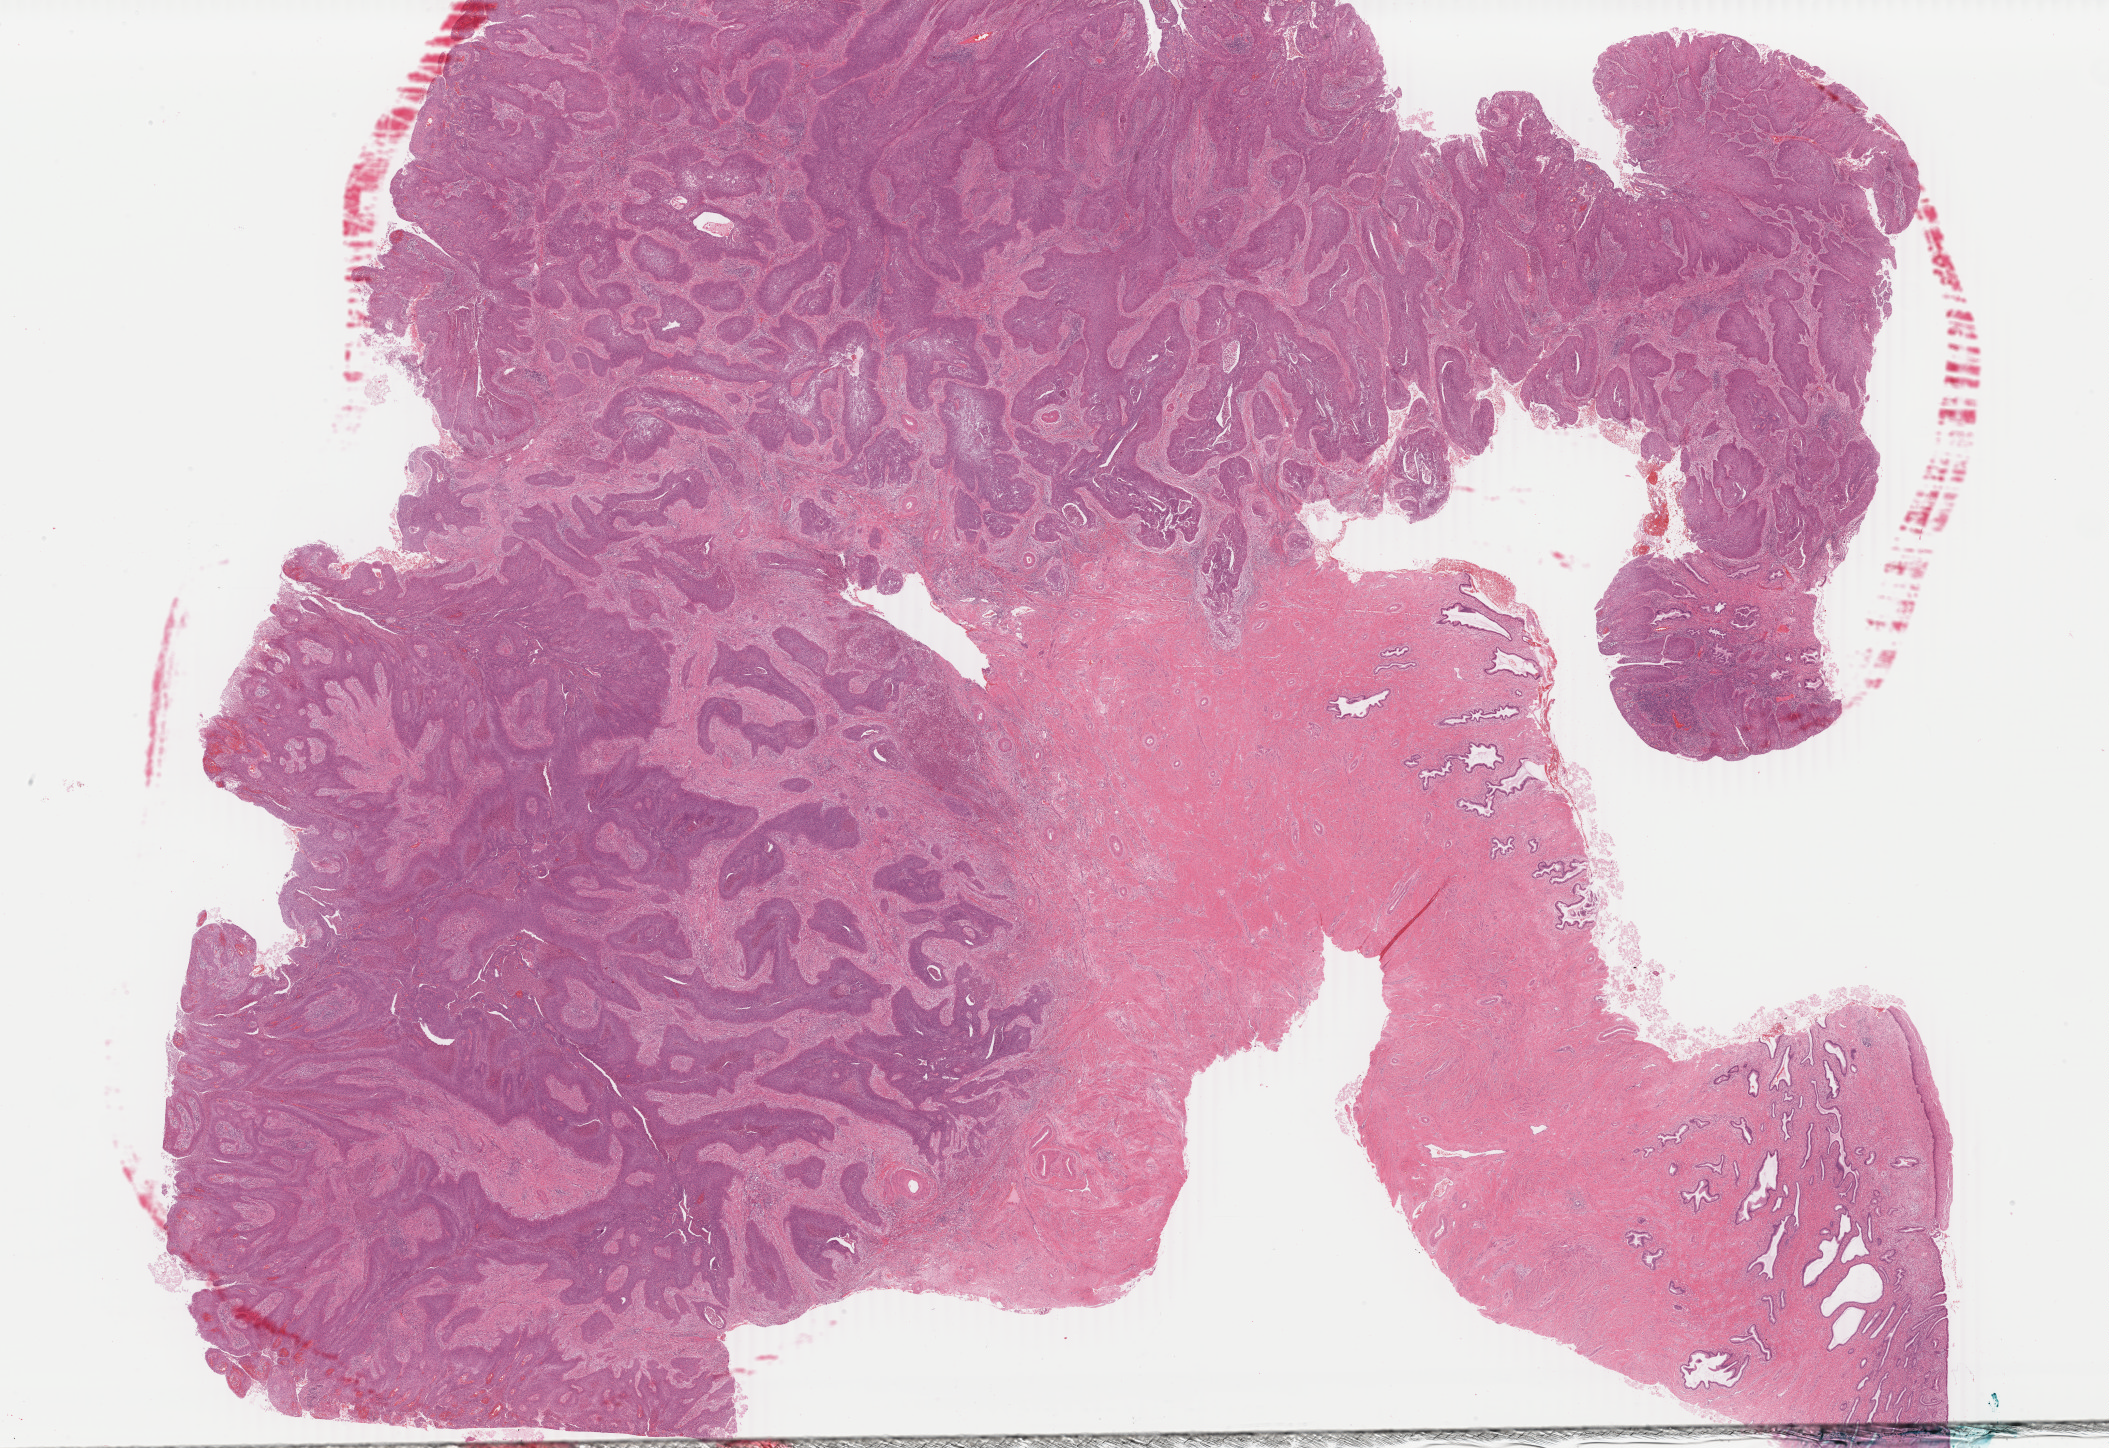
Digitized Hematoxylin and eosin (H&E) stained tissue section (whole slide) — whole scanned area (about 33.6 x 23.0 mm) shown as a low-resolution overview; FFPE section; sample: primary tumour, cervix. Female, age 40 years at initial diagnosis. Histologic grade: G2 (moderately differentiated).
* histologic diagnosis: Squamous cell carcinoma, NOS (cervix uteri)
* FIGO stage: IB1